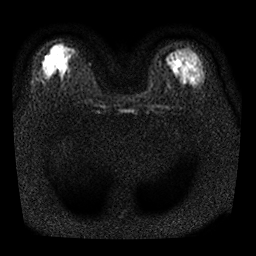
Breast MRI, one axial slice. Slice 16 of 25 in the series (ordered by position). Diffusion-weighted series; image 2 of 4 stored at this slice position (different b-values; order by instance number). 1.5 T. 4 mm slice thickness. 256 × 256 image matrix, field of view 310 × 310 mm. Female patient.
Annotated regions visible in this slice (expert manual segmentation):
- tumour on diffusion-weighted imaging: box from (x=46, y=62) to (x=52, y=68) px